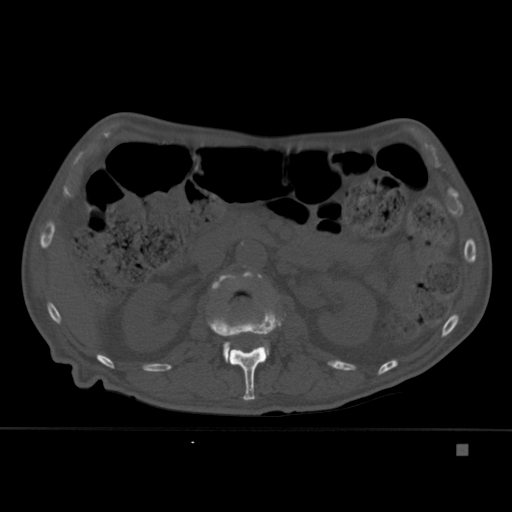
CT including the spine, one axial slice; position 176 of 451 along the scan axis; bone window (W 1800 / L 400 HU); 512 × 512 image matrix, field of view 378 × 378 mm. Patient: male, 75 years. Case-level facts recorded for this patient, not image findings: primary cancer: prostate.
Structures marked on this image (semi-automatically segmented with operator editing):
- L1 vertebra: bounding box <208,305,286,401> (left, top, right, bottom; pixels)
- L2 vertebra: <212,271,269,363>